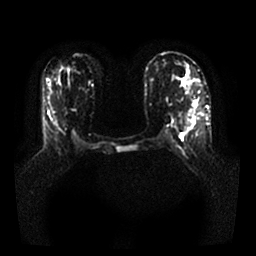
Breast MRI, one axial slice. Diffusion-weighted series; image 2 of 4 stored at this slice position (different b-values; order by instance number). 1.5 T. 256 × 256 image matrix, field of view 340 × 340 mm. Female patient.
Structures marked on this image (manually delineated by an expert):
- tumour on diffusion-weighted imaging: bounding box (x1, y1, x2, y2) in pixels: (193, 101, 198, 108)